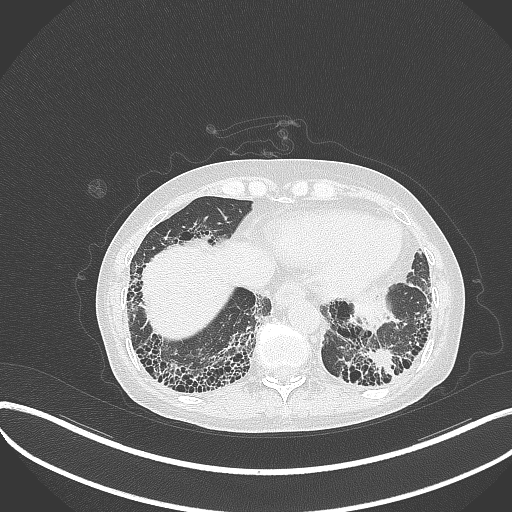
Chest CT, one axial slice; position 66 of 373 along the scan axis; 120 kVp; lung window (W 1500 / L -600 HU); 512 × 512 image matrix. Patient: female, 56 years. Case-level facts recorded for this patient, not image findings: clinical TNM (as recorded): T1 N0 M0.
Structures marked on this image (bounding box drawn by a radiologist):
- lung tumour (recorded histology: adenocarcinoma): bounding box (x1, y1, x2, y2) in pixels: (365, 346, 404, 383)